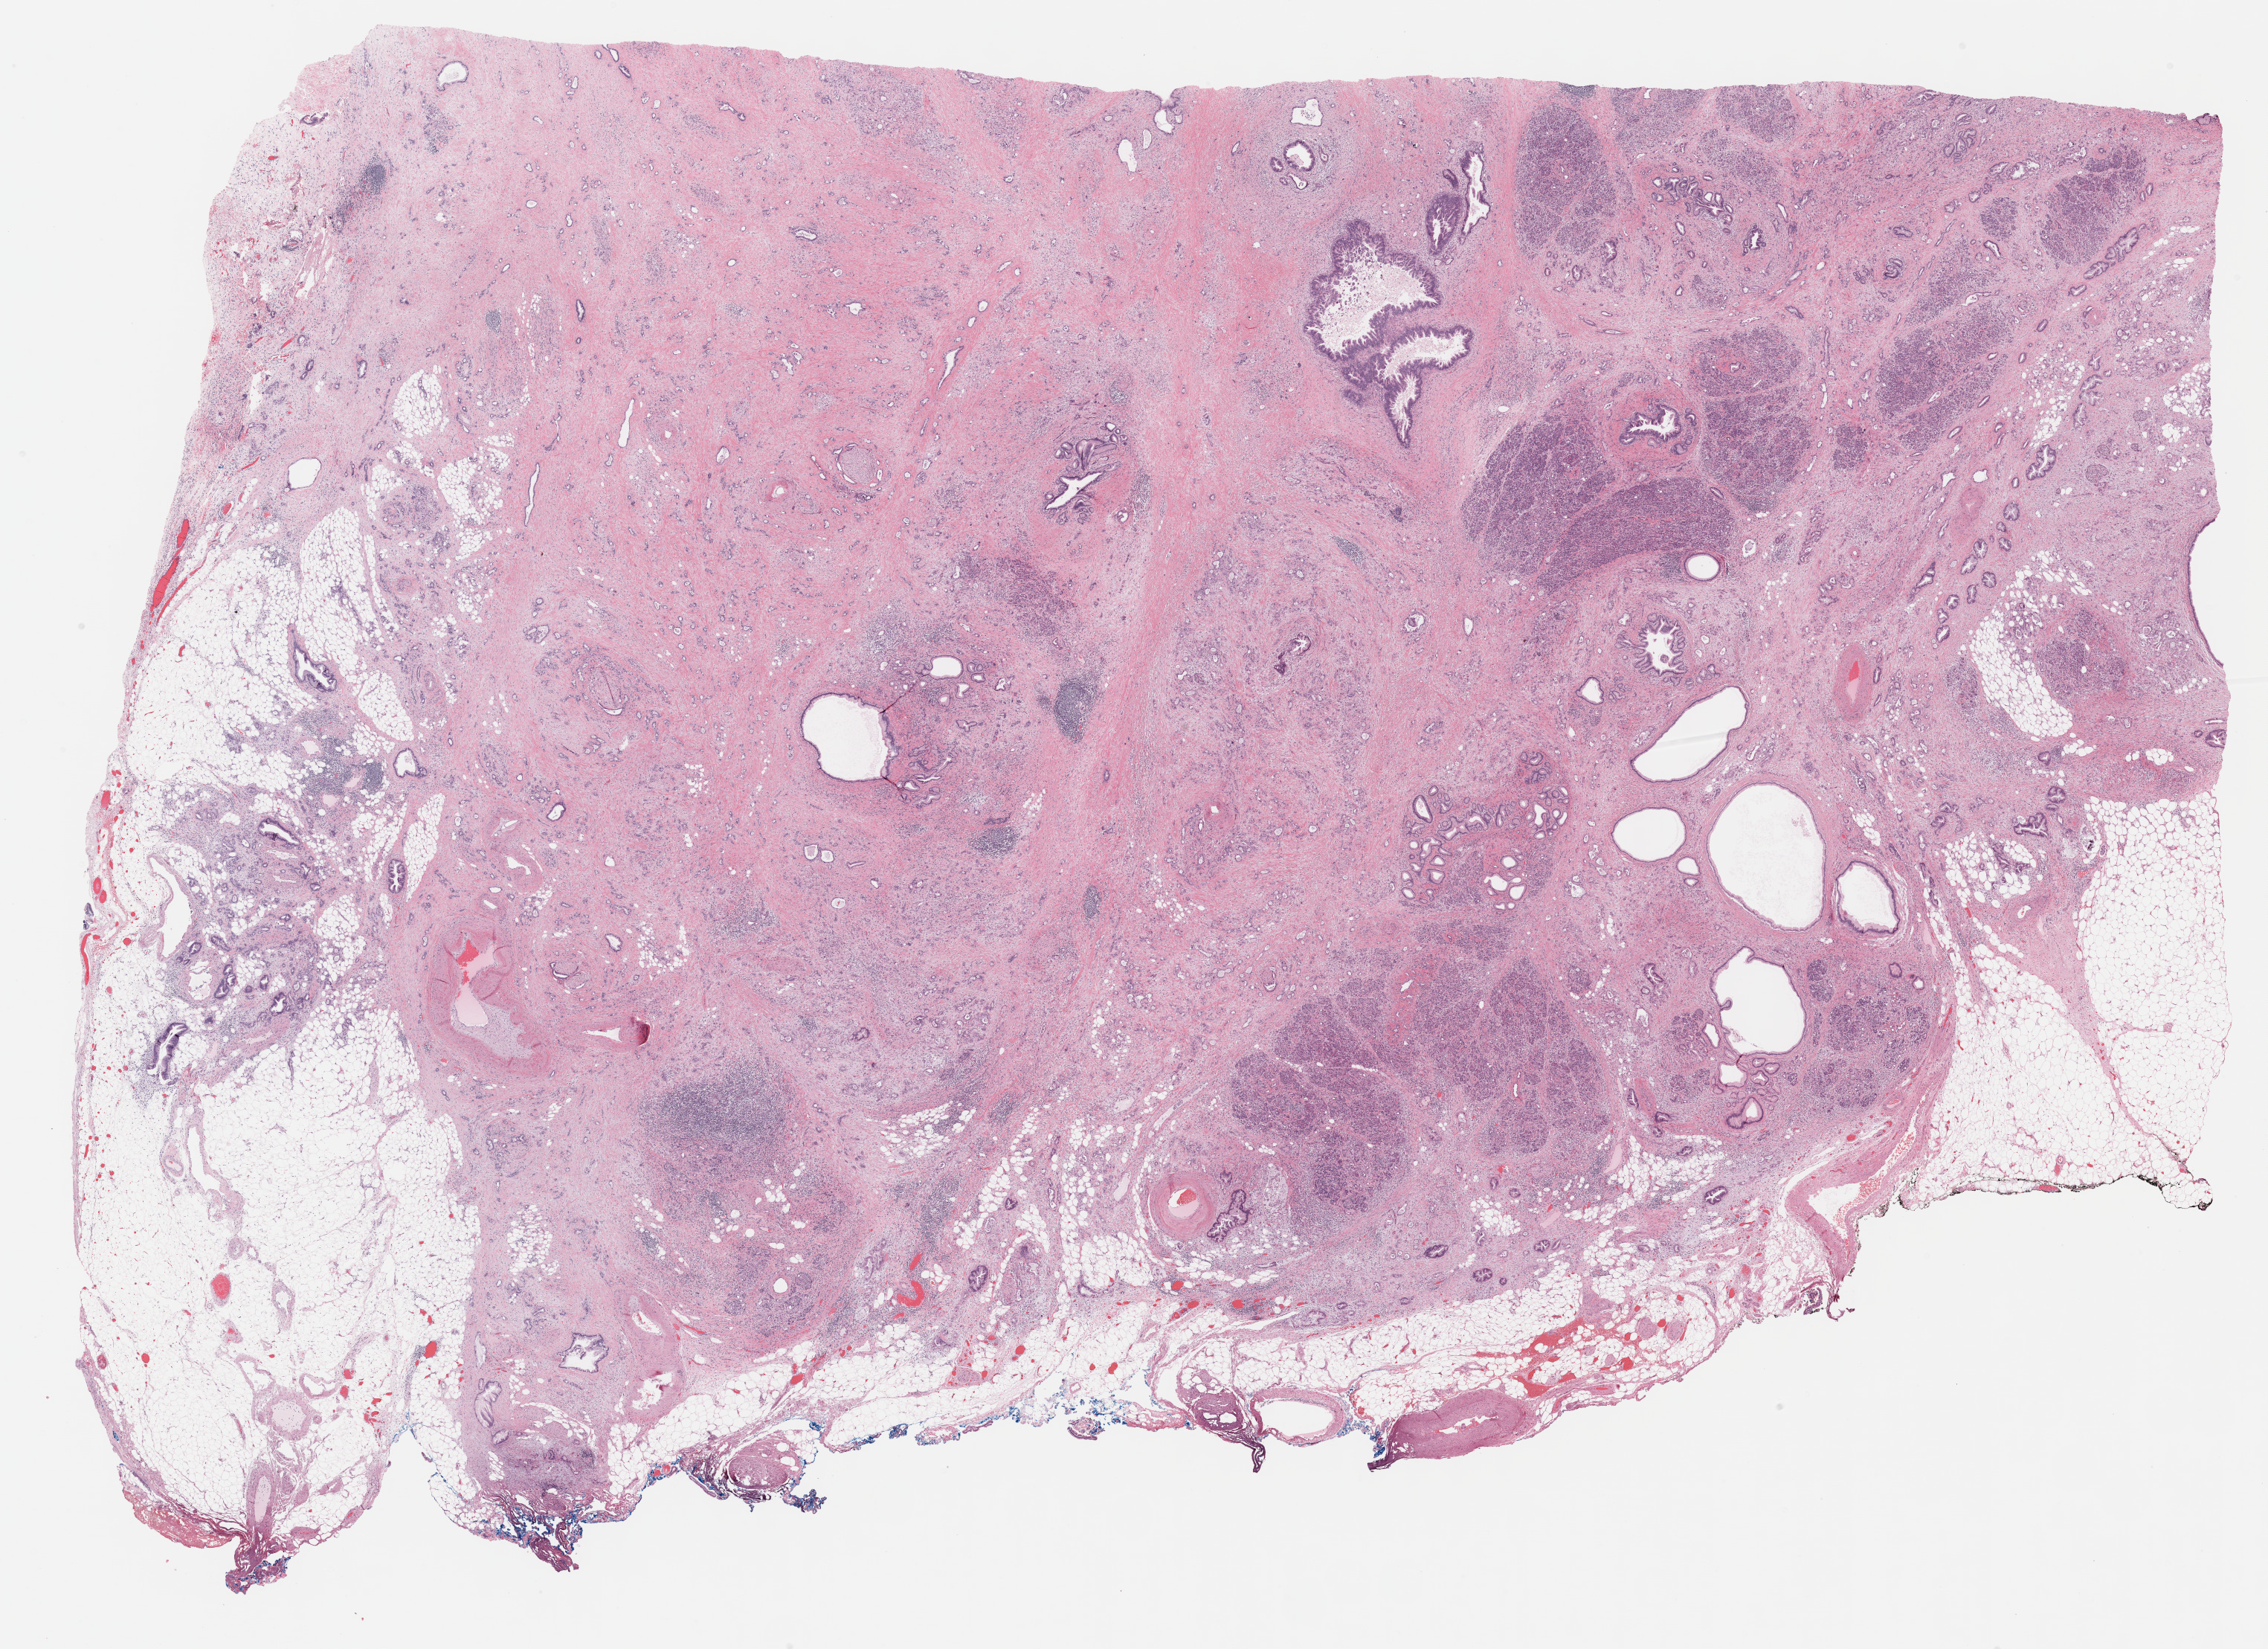
Digitized Hematoxylin and eosin (H&E) stained tissue section (whole slide) — low-resolution overview of the scanned area, about 24.7 x 17.9 mm (acquisition: 40x scan). Formalin-fixed paraffin-embedded (FFPE) diagnostic section. Primary tumour sample from the pancreas. Patient: female, age at initial diagnosis 85 years. Histologic grade: G1 (well differentiated).
• pathologic diagnosis: Infiltrating duct carcinoma, NOS
• AJCC pathologic stage: IIB (7th edition)
• lymph nodes positive (case pathology): 3 of 13 examined